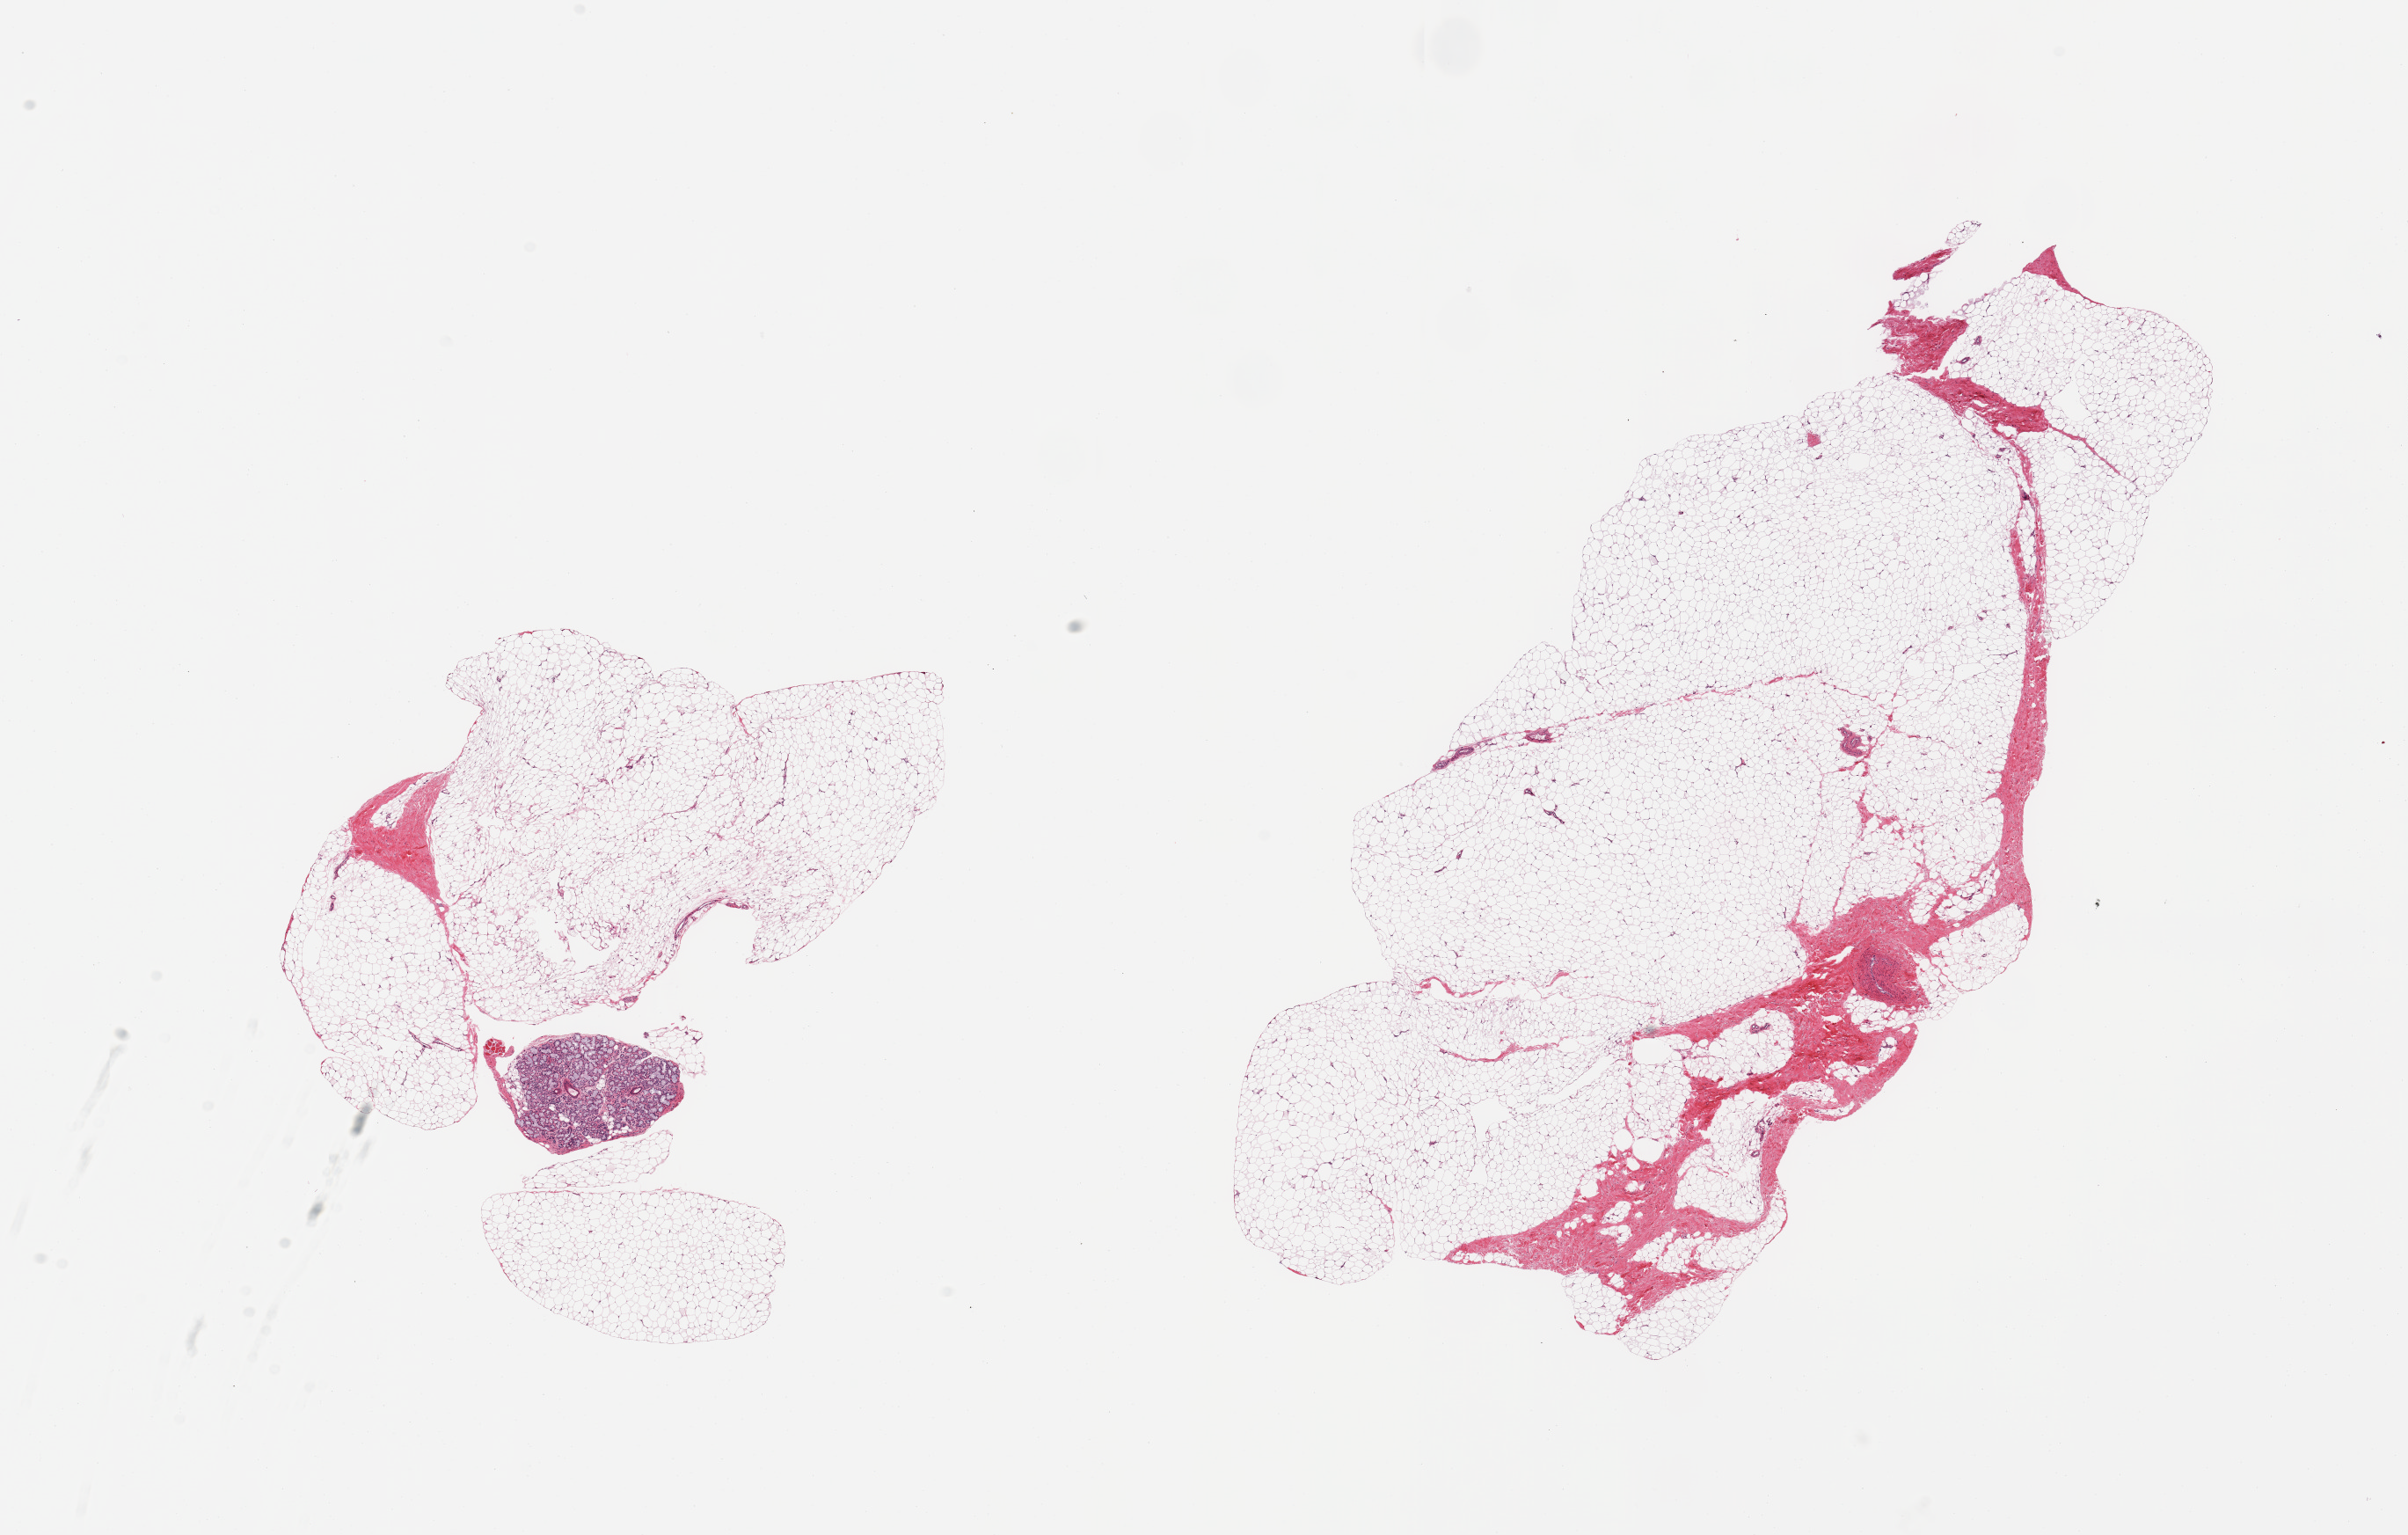
Whole-slide image, haematoxylin and eosin stain — a low-resolution overview of the entire scanned area, about 21.7 x 13.8 mm (acquisition: 20x scan); PAXgene-fixed, paraffin-embedded tissue; section of breast (target tissue); donor tissue sample. Donor sex: male.
Review note (as recorded): 2 pieces; mainly mature adipose tissue with 5% and 15% of fibrovascular component; no mammary ducts; separate 1.5 mm mucous gland (salivary) lobule with tiny fragment of skeletal muscle consistent with carry-over from 0625.